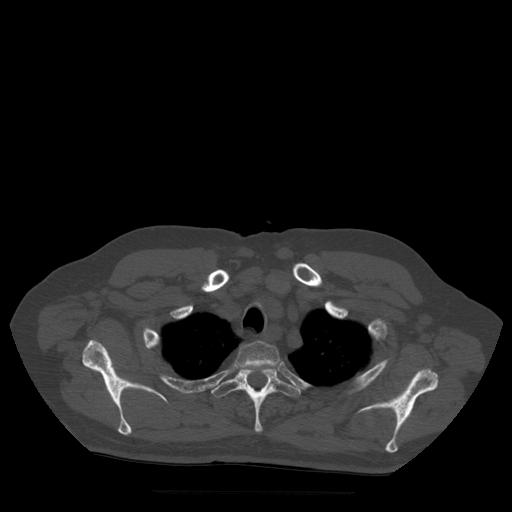
CT including the spine, one axial slice. Position 414 of 522 along the scan axis. Bone window (W 1800 / L 400 HU). 1.25 mm slice thickness. 512 × 512 image matrix, field of view 420 × 420 mm. Patient age 72 years. Case-level facts recorded for this patient, not image findings: primary cancer: prostate.
Annotated regions visible in this slice (semi-automatic segmentation, software-assisted and operator-edited):
- T2 vertebra: bounding box <236,342,280,370> (left, top, right, bottom; pixels)
- T3 vertebra: <212,364,302,433>